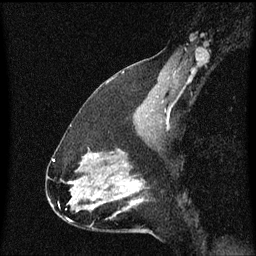
Breast MRI (dynamic contrast-enhanced), one sagittal slice; position 40 of 60 along the scan axis; dynamic contrast-enhanced series, image 2 of 3 at this slice position (ordered by acquisition); 1.5 T; TE 4.2 ms, TR 8.4 ms; 256 × 256 image matrix, field of view 200 × 200 mm. Female patient, age 47 years.
Structures marked on this image (semi-automatic segmentation, software-assisted and operator-edited):
- analysis volume of interest (the breast-tissue region the enhancement analysis was run in; not a lesion): box from (x=100, y=172) to (x=147, y=219) px
- tumour enhancement mask (voxels above the 70 % enhancement threshold inside the analysis volume of interest): (x=120, y=184)–(x=142, y=205)